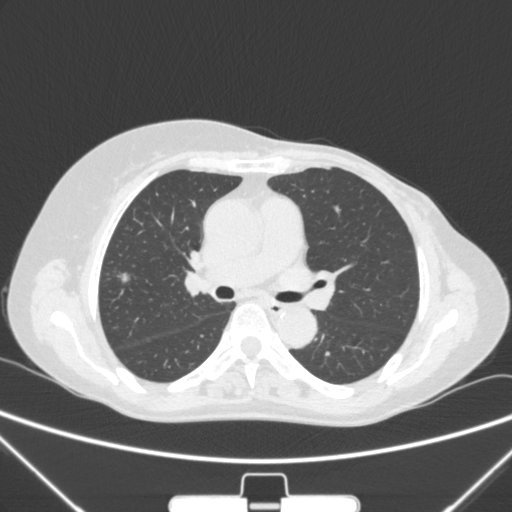
Chest CT, one axial slice; slice 151 of 265 in the series (ordered by position); 120 kVp; lung window (W 1500 / L -600 HU); 1 mm slice thickness; 512 × 512 image matrix. Female patient, age 64 years. Case-level facts recorded for this patient, not image findings: clinical TNM (as recorded): T1c N0 M0; histopathological grade: G1-2.
Annotated regions visible in this slice (bounding box drawn by a radiologist):
- lung tumour (recorded histology: adenocarcinoma): bounding box <111,265,141,299> (left, top, right, bottom; pixels)